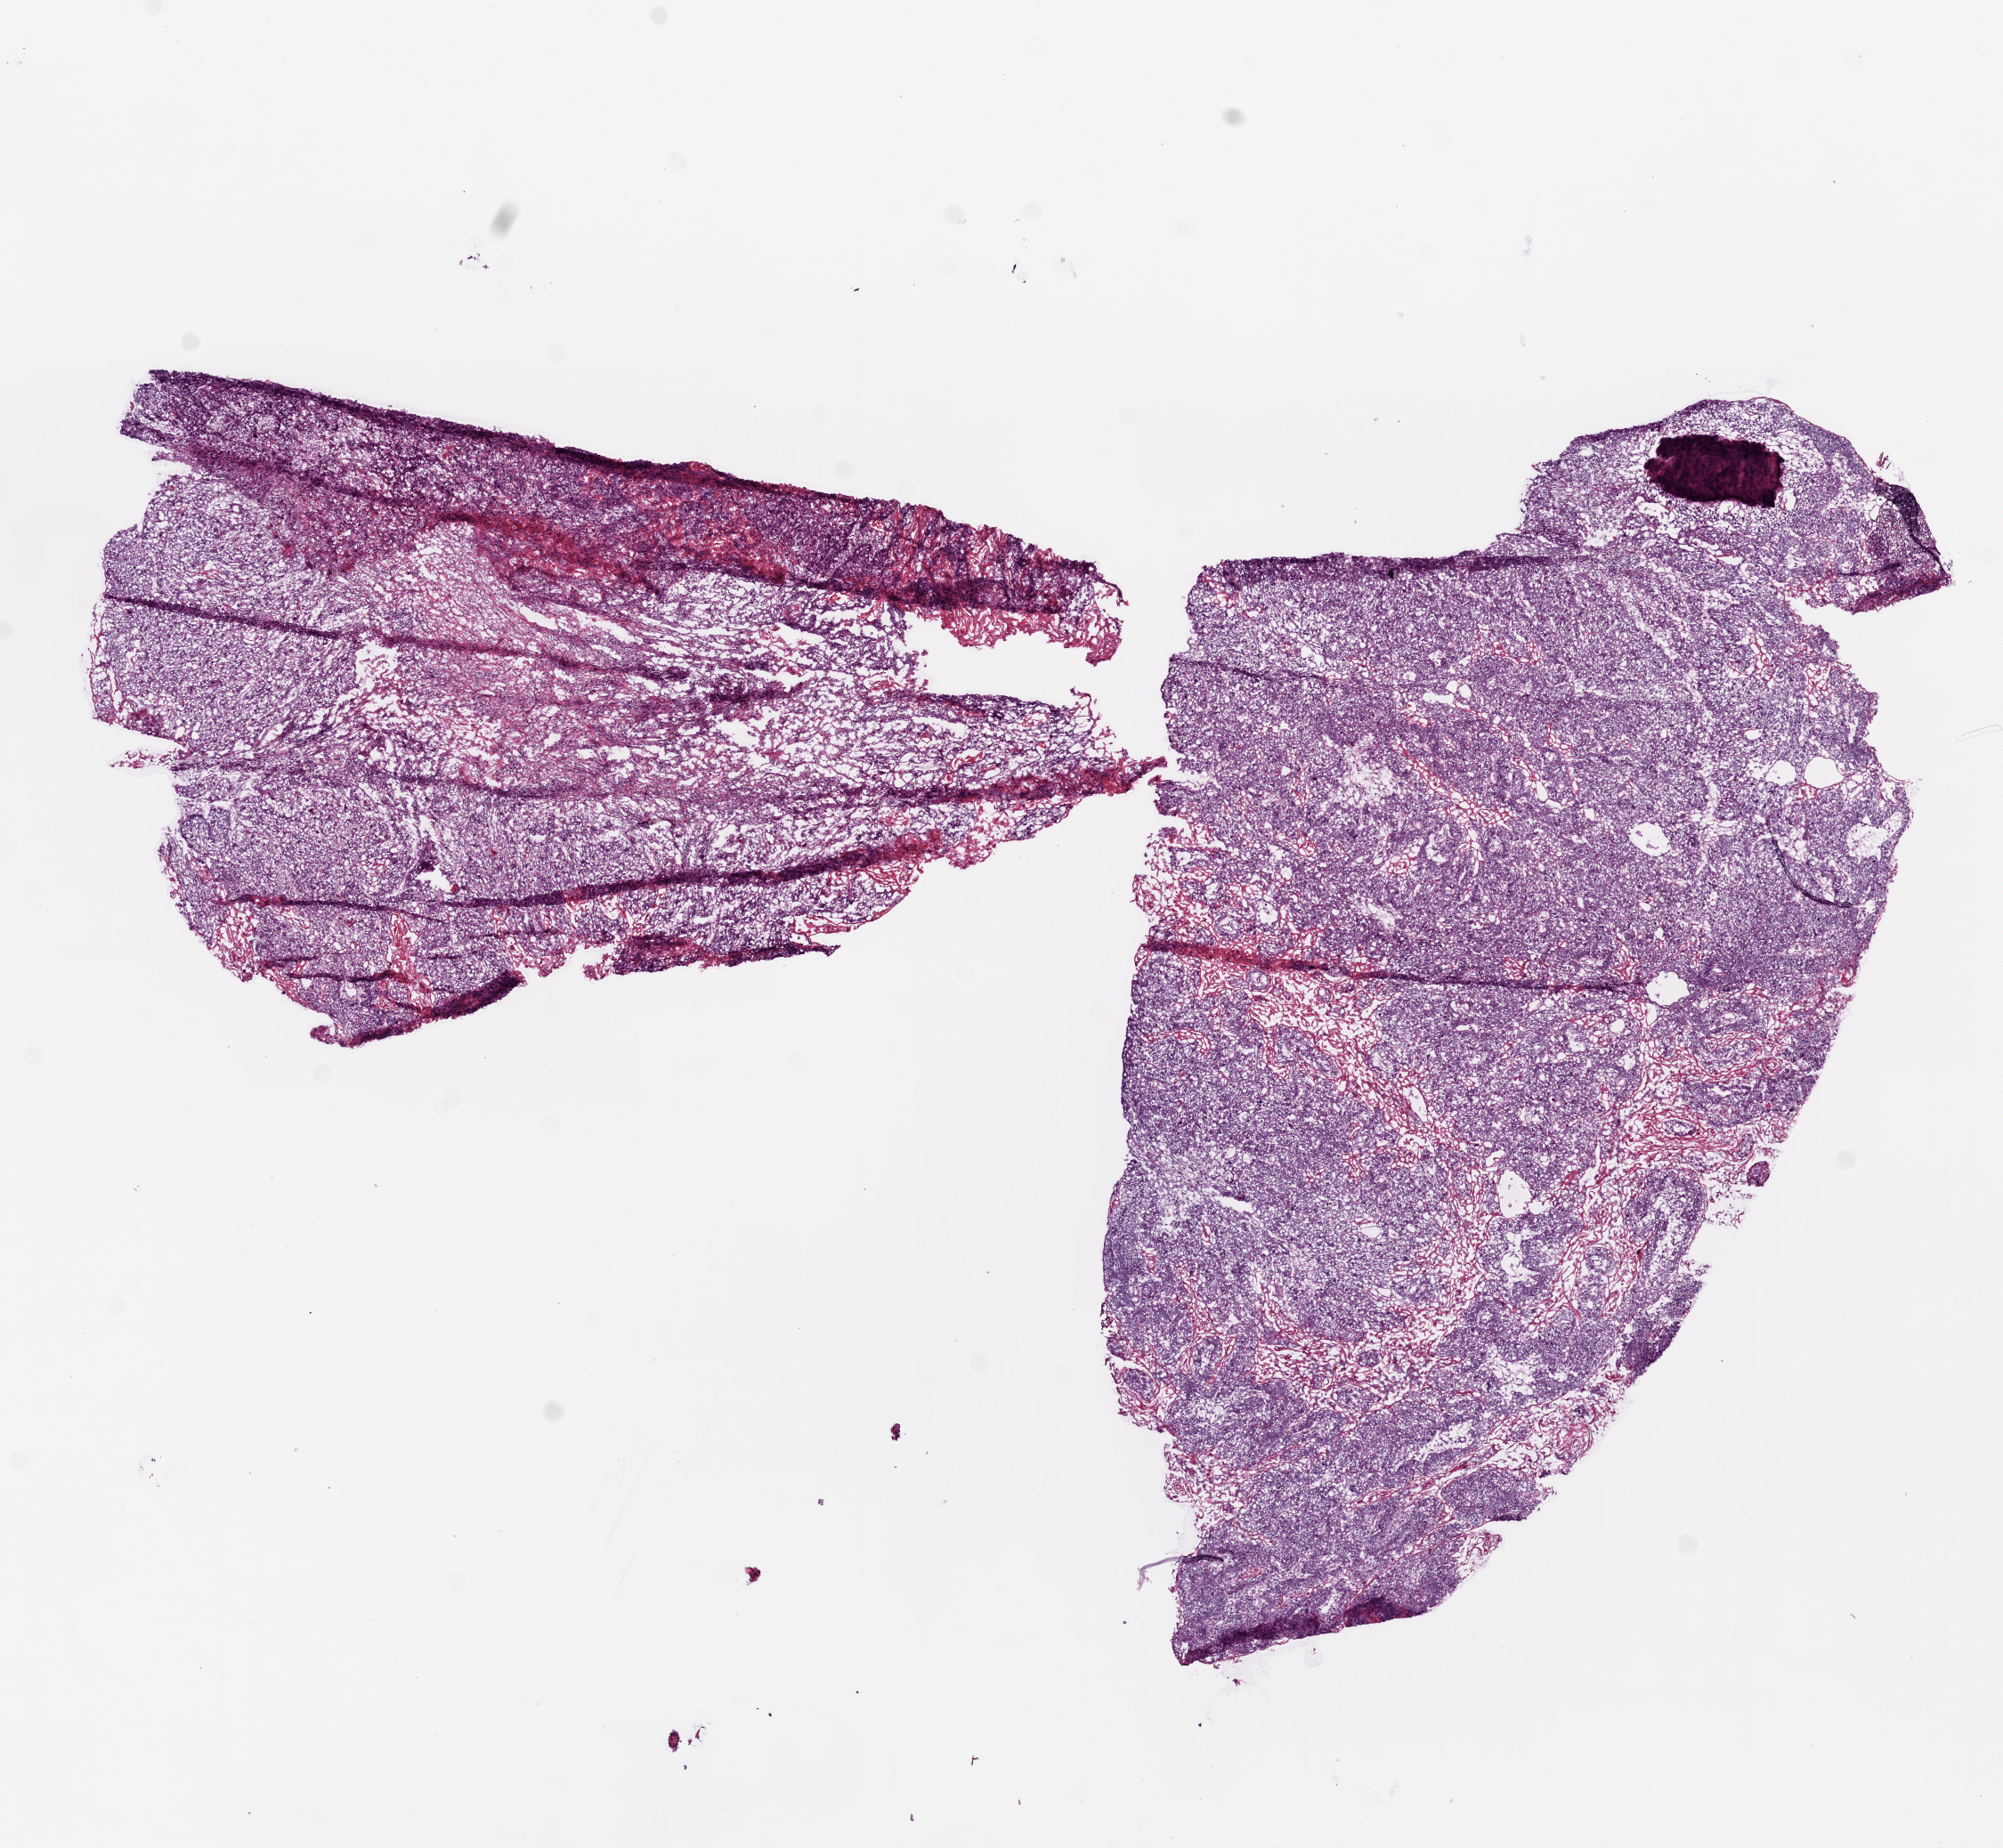
Whole-slide histology image, Hematoxylin and eosin (H&E) stained, low-resolution overview of the scanned area, about 9.0 x 8.3 mm. Frozen section. Head and neck, primary tumour sample. Patient: male, age at initial diagnosis 62 years. Histologic grade: G2 (moderately differentiated). Composition of this section per pathologist review: tumour cells 90%, tumour nuclei 85%, normal cells 0%, stromal cells 10%, necrosis 0%.
Histologic diagnosis: Squamous cell carcinoma, NOS (overlapping lesion of lip, oral cavity and pharynx). AJCC pathologic stage: IVA.